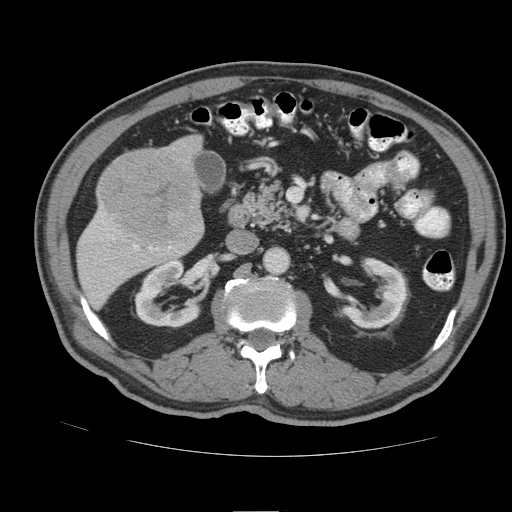
Contrast-enhanced abdominal CT (liver protocol), one axial slice. Soft-tissue window (W 400 / L 40 HU). 2.5 mm slice thickness. 512 × 512 image matrix, field of view 380 × 380 mm. Case-level facts recorded for this patient, not image findings: diagnosis: hepatocellular carcinoma (patient treated with transarterial chemoembolisation; whether this scan precedes or follows treatment is not stated here); TNM stage (as recorded): Stage-IIIB; Child-Pugh class: A; tumour nodularity: multinodular.
Outlined on this slice (semi-automatically segmented with operator editing):
- liver parenchyma outside the tumour (the mass and vessels are separate outlines, so this box may not span the whole liver): bounding box <76,134,204,308> (left, top, right, bottom; pixels)
- mass: <100,151,198,243>
- liver vessels: <112,237,171,250>